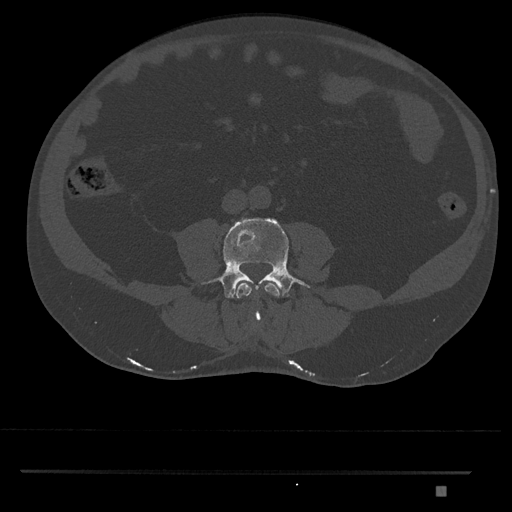
CT including the spine, one axial slice; position 635 of 1134 along the scan axis; bone window (W 1800 / L 400 HU); 512 × 512 image matrix, field of view 429 × 429 mm. Patient: male, 65 years. From the clinical record (not read from this slice): primary cancer: prostate.
Annotated regions visible in this slice (semi-automatically segmented with operator editing):
- L3 vertebra: bounding box <236,282,280,323> (left, top, right, bottom; pixels)
- L4 vertebra: <202,218,310,298>